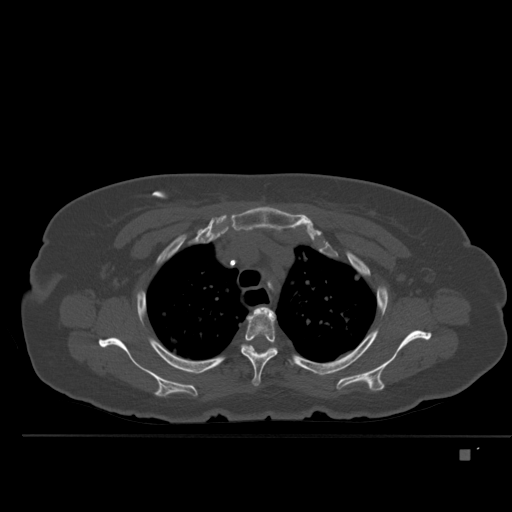
CT including the spine, one axial slice. Slice 378 of 477 in the series (ordered by position). Bone window (W 1800 / L 400 HU). 512 × 512 image matrix. Female patient, age 74 years. From the clinical record (not read from this slice): primary cancer: colon.
Structures marked on this image (semi-automatic segmentation, software-assisted and operator-edited):
- T2 vertebra: bounding box <262,307,266,310> (left, top, right, bottom; pixels)
- T3 vertebra: <241,306,278,386>
- T4 vertebra: <224,344,256,358>